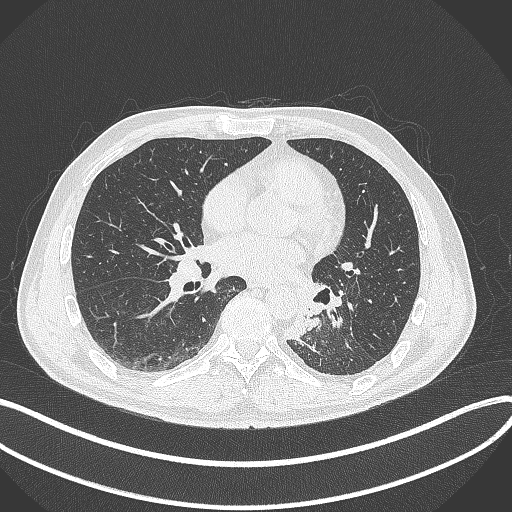
Chest CT, one axial slice; position 144 of 329 along the scan axis; 120 kVp; lung window (W 1500 / L -600 HU); 512 × 512 image matrix, field of view 400 × 400 mm. Patient: male, 59 years. From the clinical record (not read from this slice): clinical TNM (as recorded): T2a N2 M0.
Structures marked on this image (rectangle marked by the reading radiologist):
- lung tumour (recorded histology: squamous cell carcinoma): box from (x=277, y=310) to (x=323, y=343) px